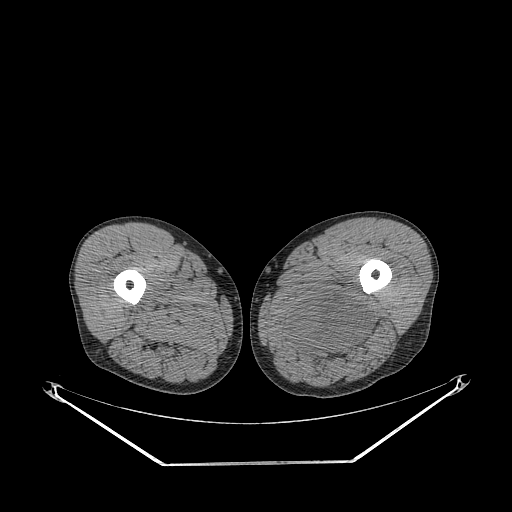
CT of an extremity soft-tissue mass (from a PET/CT study), one axial slice; slice 254 of 267 in the series (ordered by position); 140 kVp; soft-tissue window (W 400 / L 40 HU); 3.75 mm slice thickness; 512 × 512 image matrix. Male patient. From the clinical record (not read from this slice): histological type: undifferentiated pleomorphic liposarcoma; grade: high; site of the primary tumour: left thigh.
Outlined on this slice (expert contour drawn on MRI and transferred to this co-registered scan by the dataset authors):
- gross tumour volume including surrounding oedema: bounding box [x1, y1, x2, y2] px = [281, 290, 369, 359]
- gross tumour volume (mass): [290, 294, 366, 352]